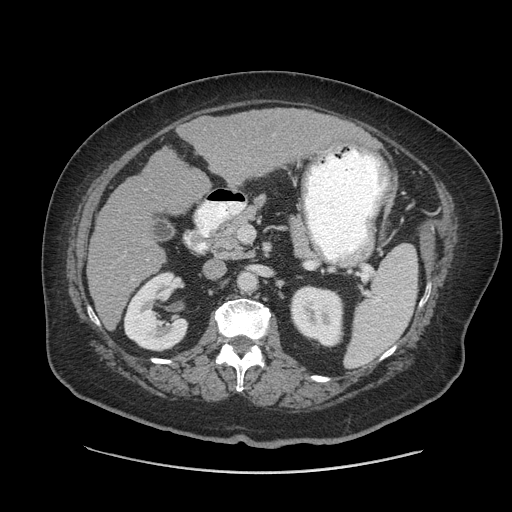
Contrast-enhanced abdominal CT (liver protocol), one axial slice. Position 31 of 91 along the scan axis. Reconstruction kernel STANDARD. Soft-tissue window (W 400 / L 40 HU). 2.5 mm slice thickness. 512 × 512 image matrix, field of view 420 × 420 mm. From the clinical record (not read from this slice): diagnosis: hepatocellular carcinoma (patient treated with transarterial chemoembolisation; whether this scan precedes or follows treatment is not stated here); TNM stage (as recorded): Stage-I; Child-Pugh class: A; tumour differentiation: well differentiated.
Outlined on this slice (semi-automatically segmented with operator editing):
- liver parenchyma outside the tumour (the mass and vessels are separate outlines, so this box may not span the whole liver): bounding box (x1, y1, x2, y2) in pixels: (86, 108, 370, 329)